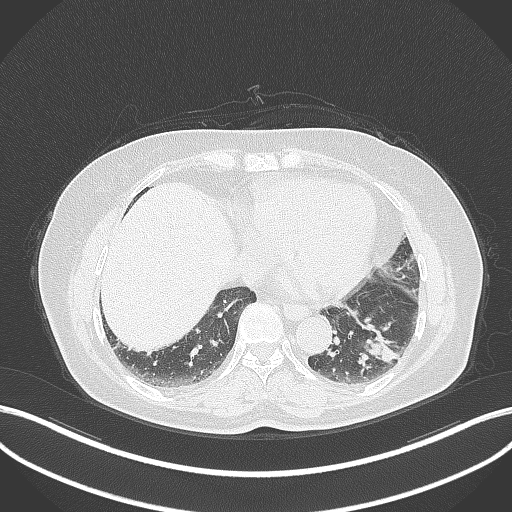
Chest CT, one axial slice; reconstruction kernel B70f; lung window (W 1500 / L -600 HU); 1 mm slice thickness; 512 × 512 image matrix, field of view 400 × 400 mm. Female patient, age 59 years. Case-level facts recorded for this patient, not image findings: clinical TNM (as recorded): T2a N0 M0.
Structures marked on this image (rectangle marked by the reading radiologist):
- lung tumour (recorded histology: adenocarcinoma): box from (x=351, y=319) to (x=405, y=371) px